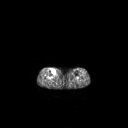
FDG PET of an extremity soft-tissue mass (from a PET/CT study), one axial slice; position 138 of 267 along the scan axis; 3.27 mm slice thickness; 128 × 128 image matrix. Patient: female, 65 years. Case-level facts recorded for this patient, not image findings: histological type: undifferentiated – high grade; grade: high; site of the primary tumour: right thigh.
Structures marked on this image (expert contour drawn on MRI and transferred to this co-registered scan by the dataset authors):
- gross tumour volume (mass): box from (x=51, y=69) to (x=56, y=75) px